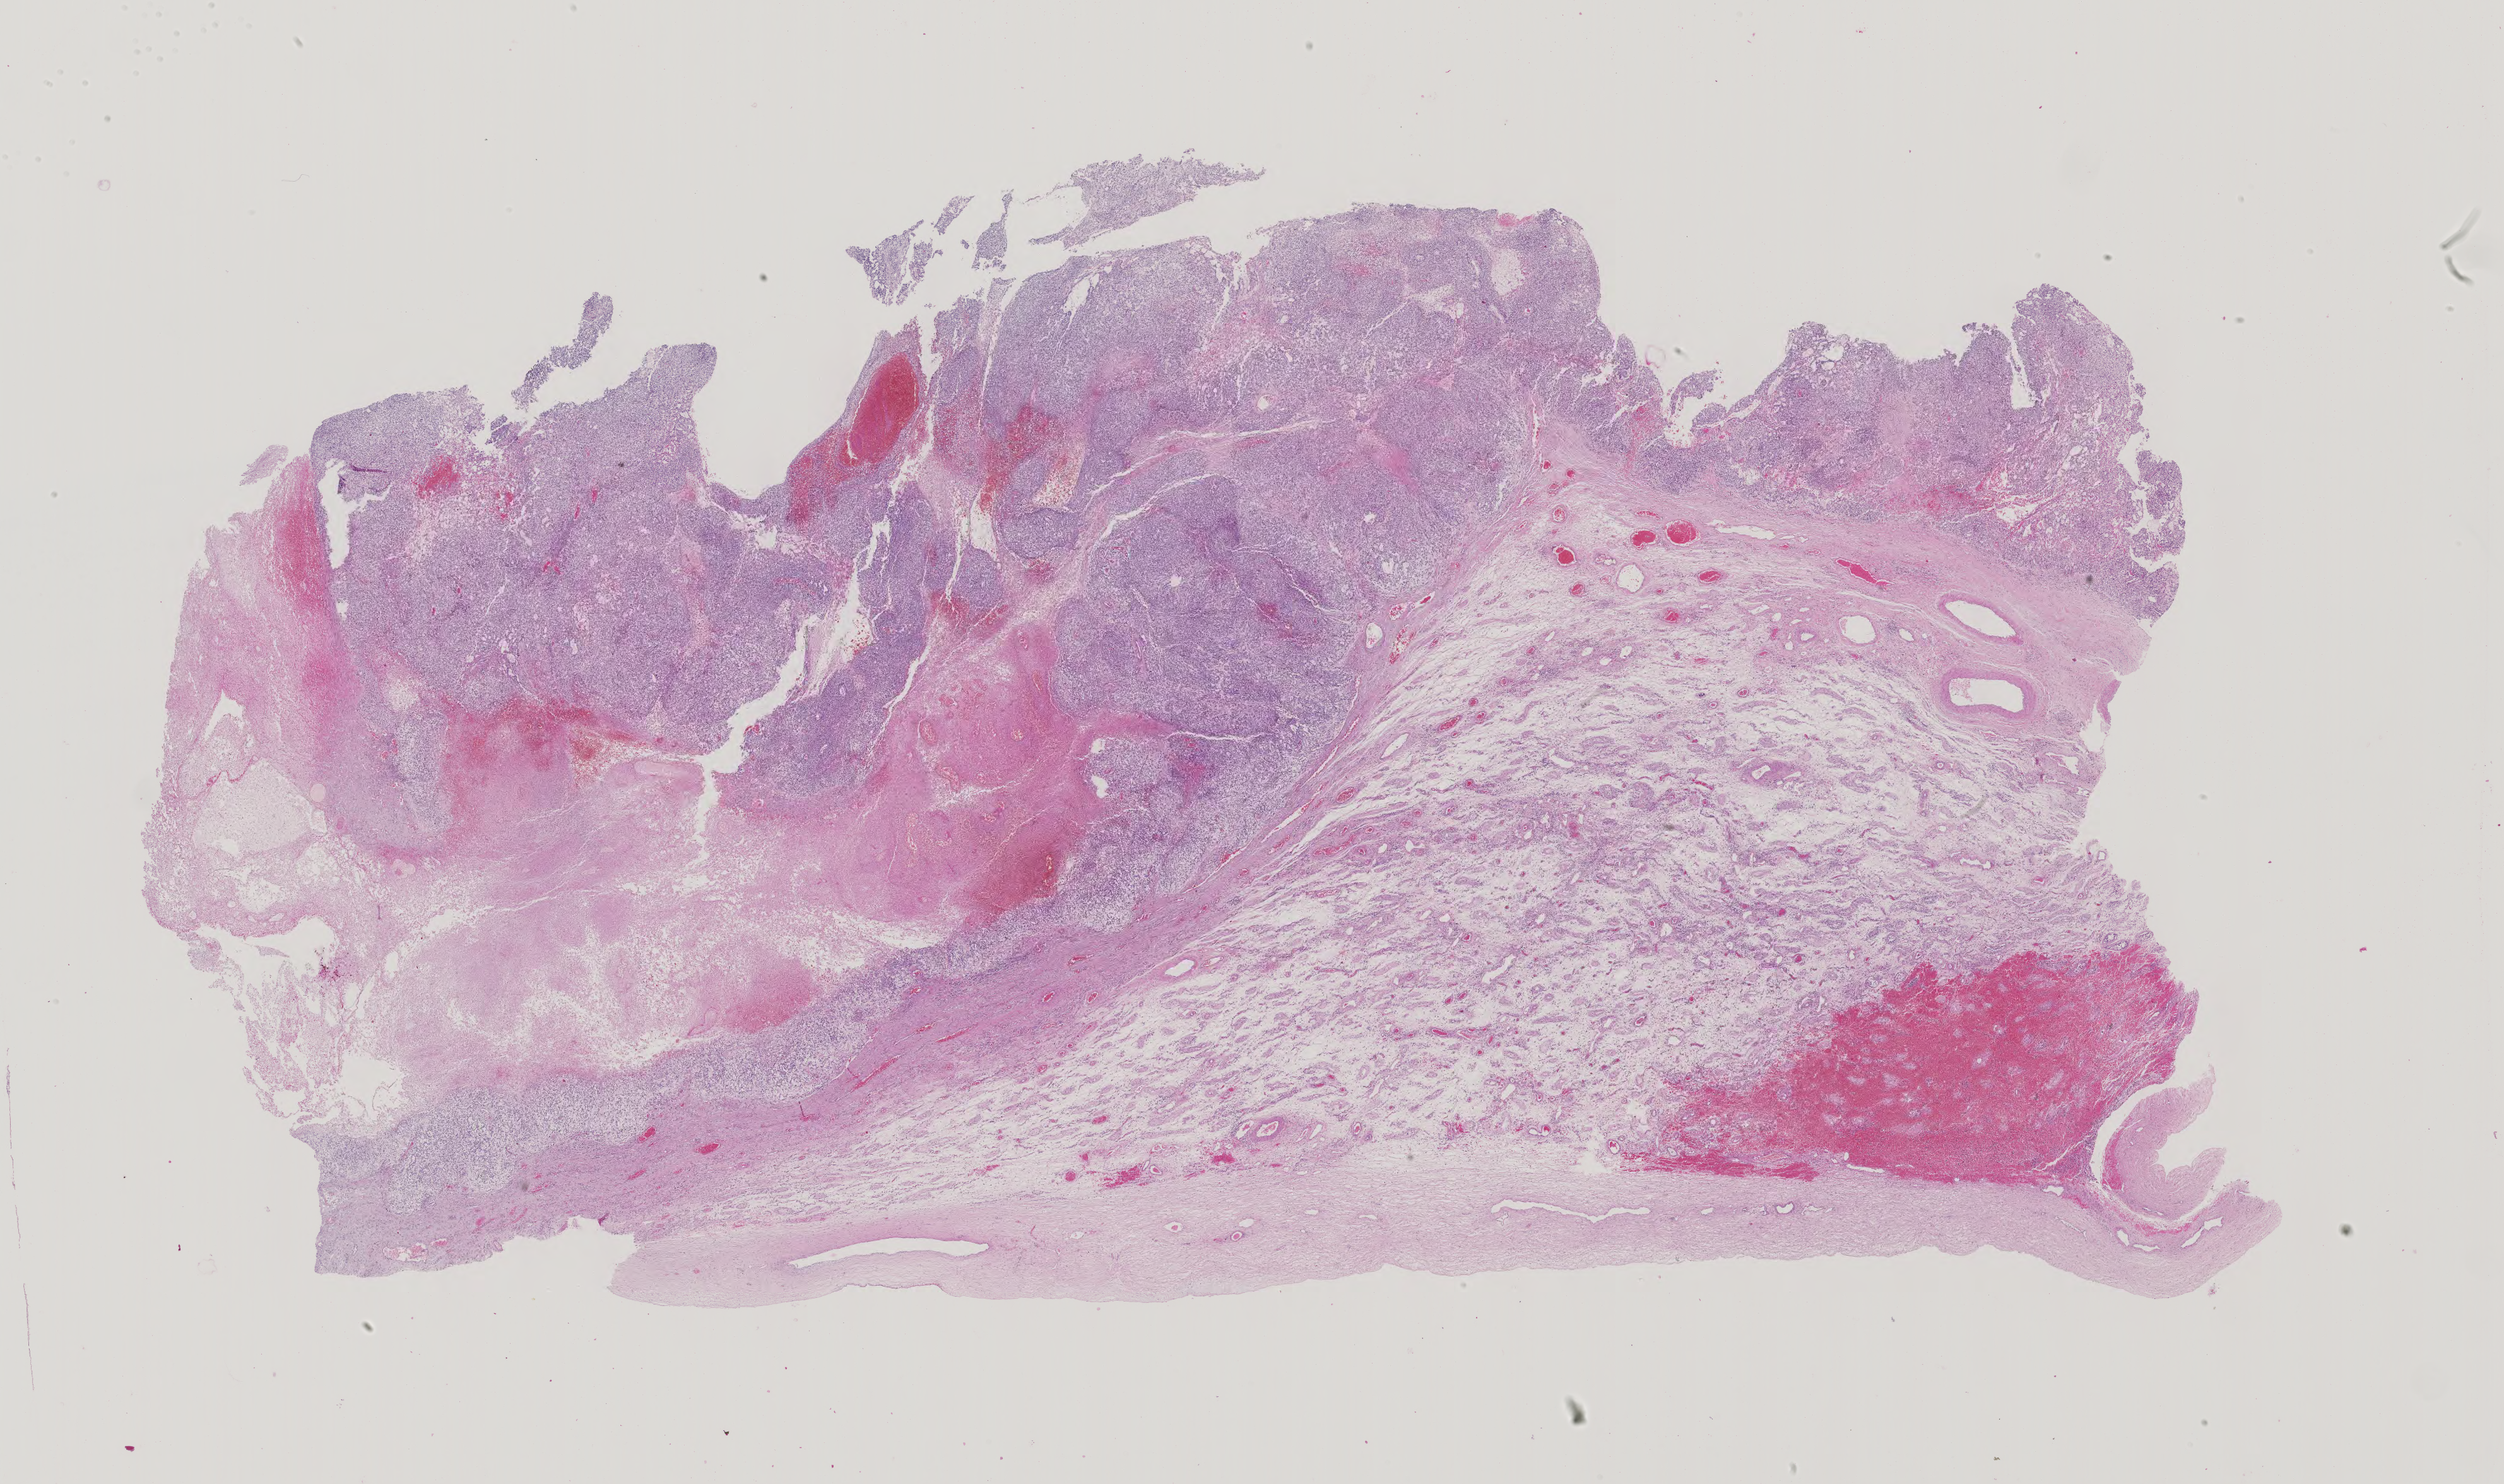
Hematoxylin and eosin (H&E) stained whole-slide image — shown as a low-resolution overview of the whole scanned area (about 28.9 x 17.1 mm, slide scanned at 40x). Male patient.
Specimen: formalin-fixed paraffin-embedded (FFPE) diagnostic section; testis, primary tumour sample.